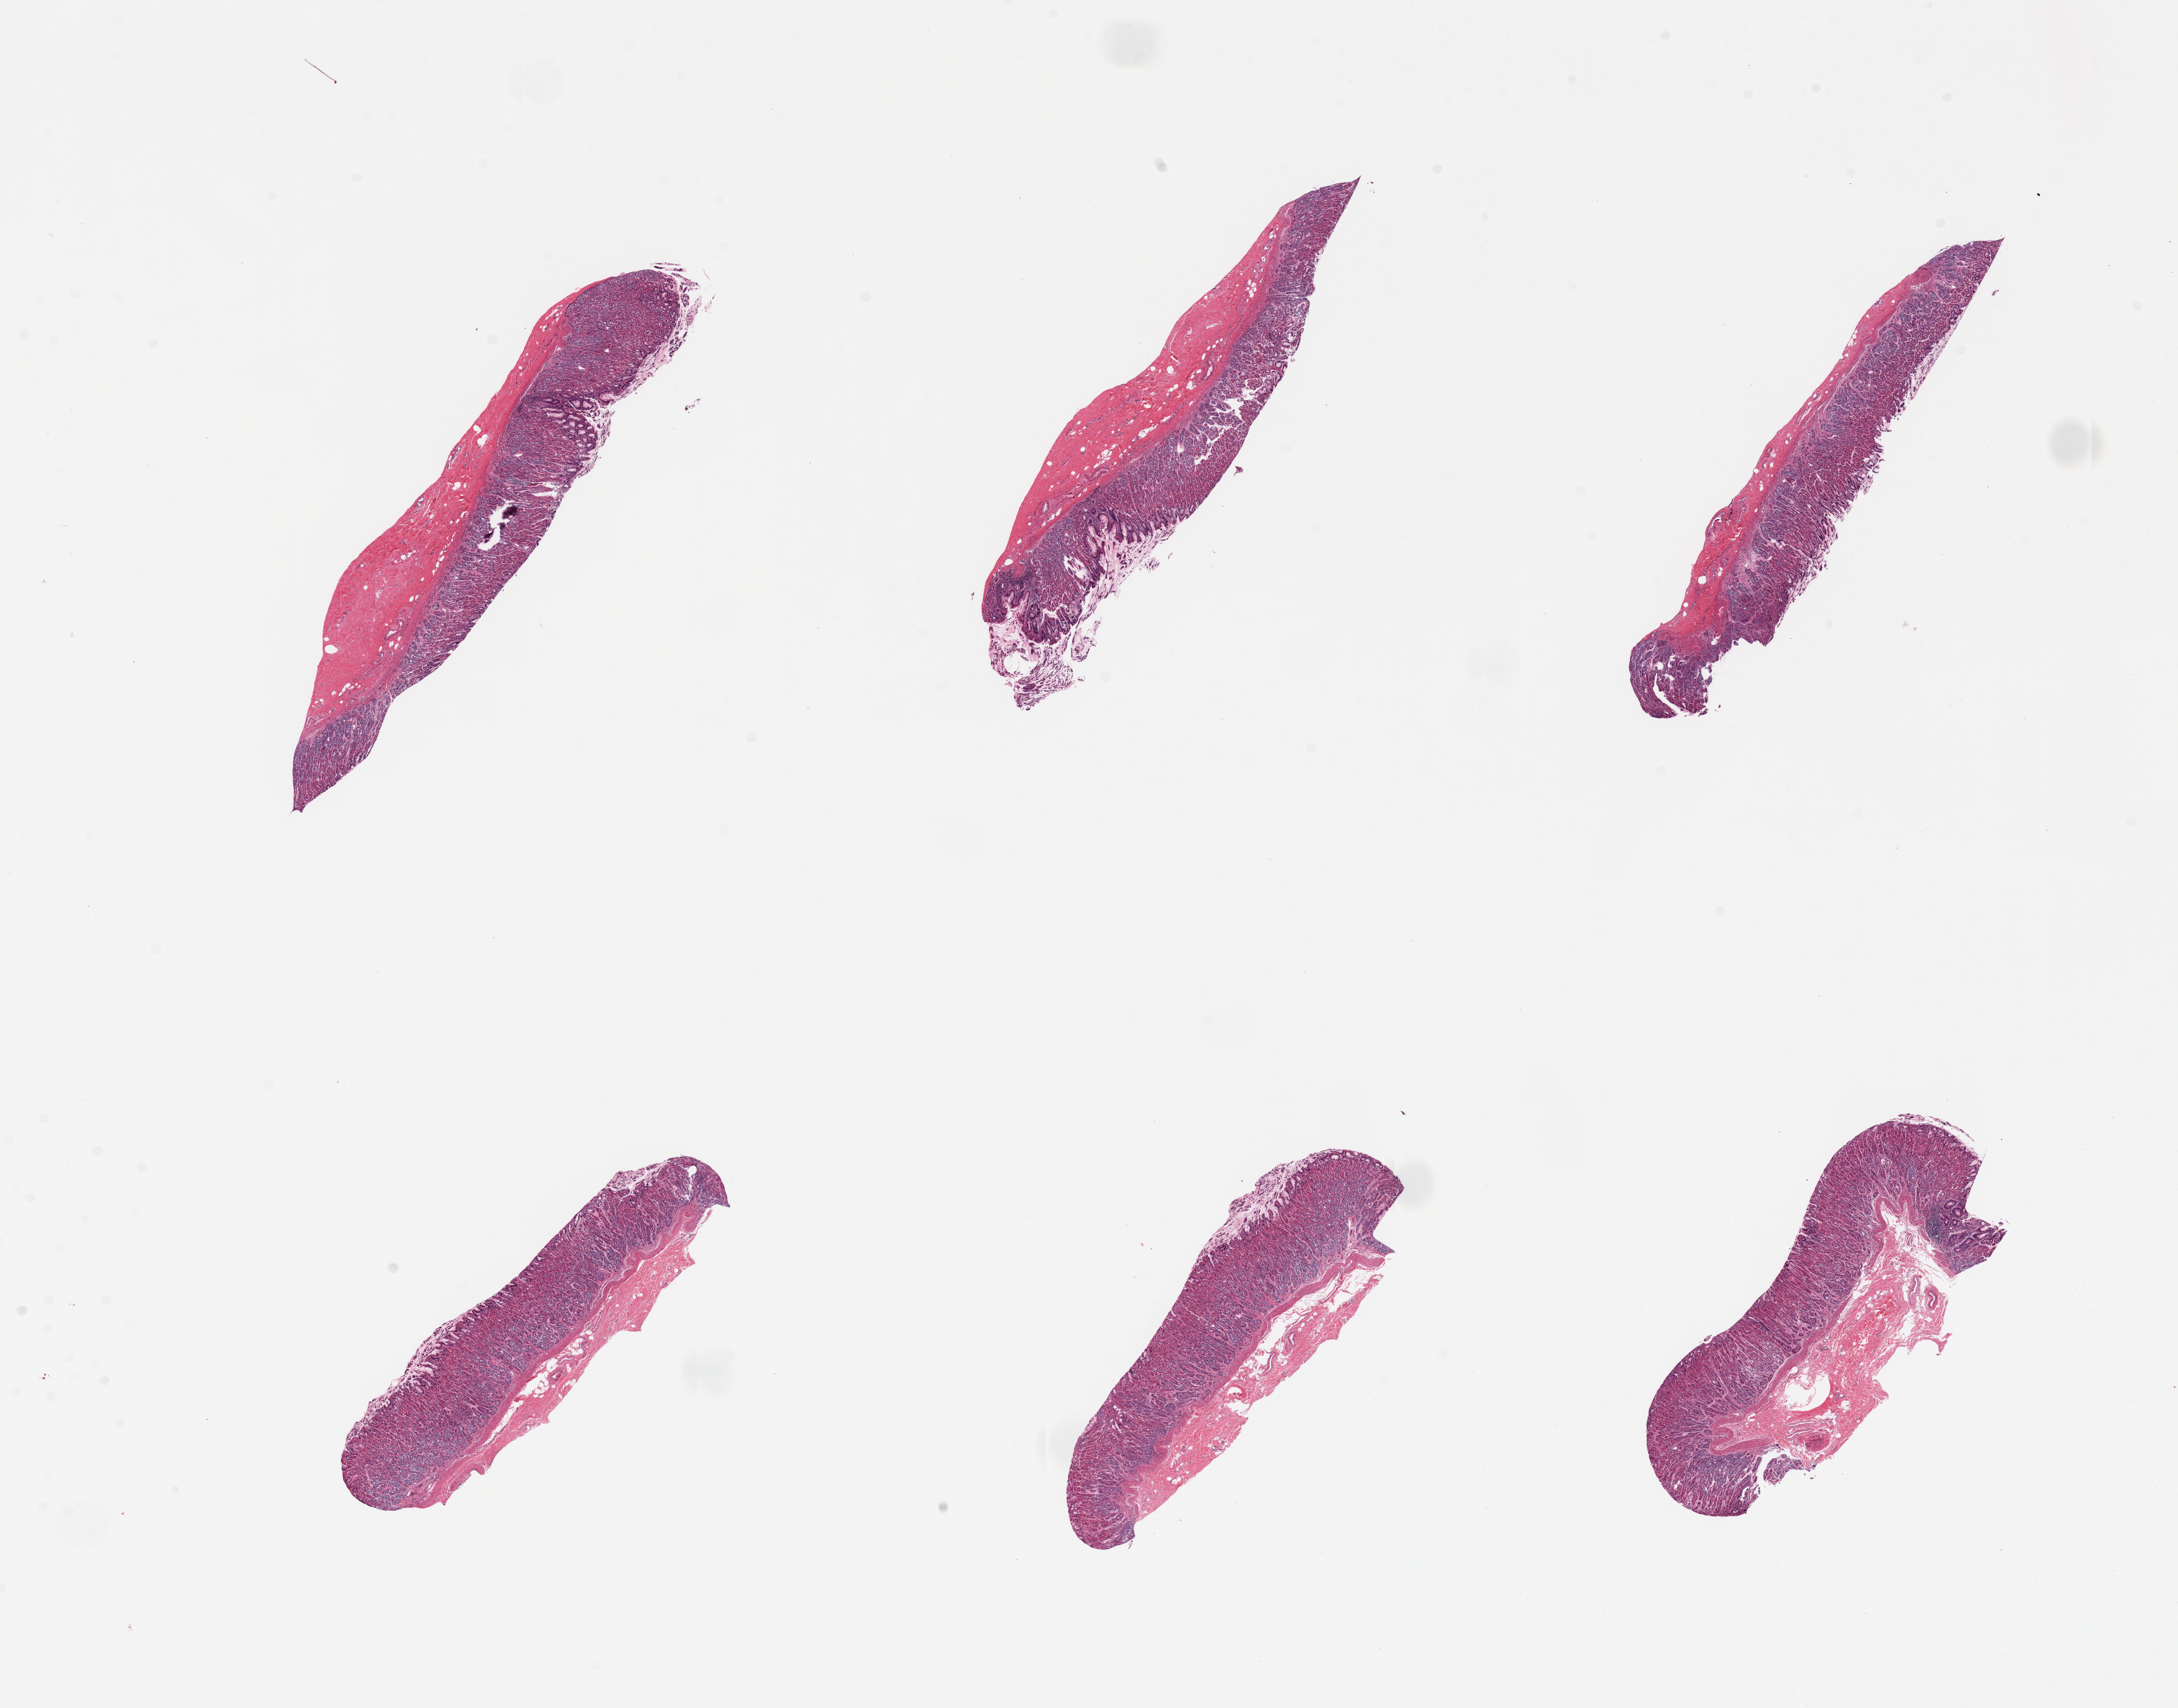
Digitized haematoxylin and eosin-stained section, brightfield, shown as a low-resolution overview of the whole scanned area (about 24.6 x 19.3 mm, acquisition: 20x scan). PAXgene-fixed paraffin-embedded (PFPE) section. Target tissue: stomach. Donor tissue sample.
Review note (as recorded): 6 pieces; mucosa only.